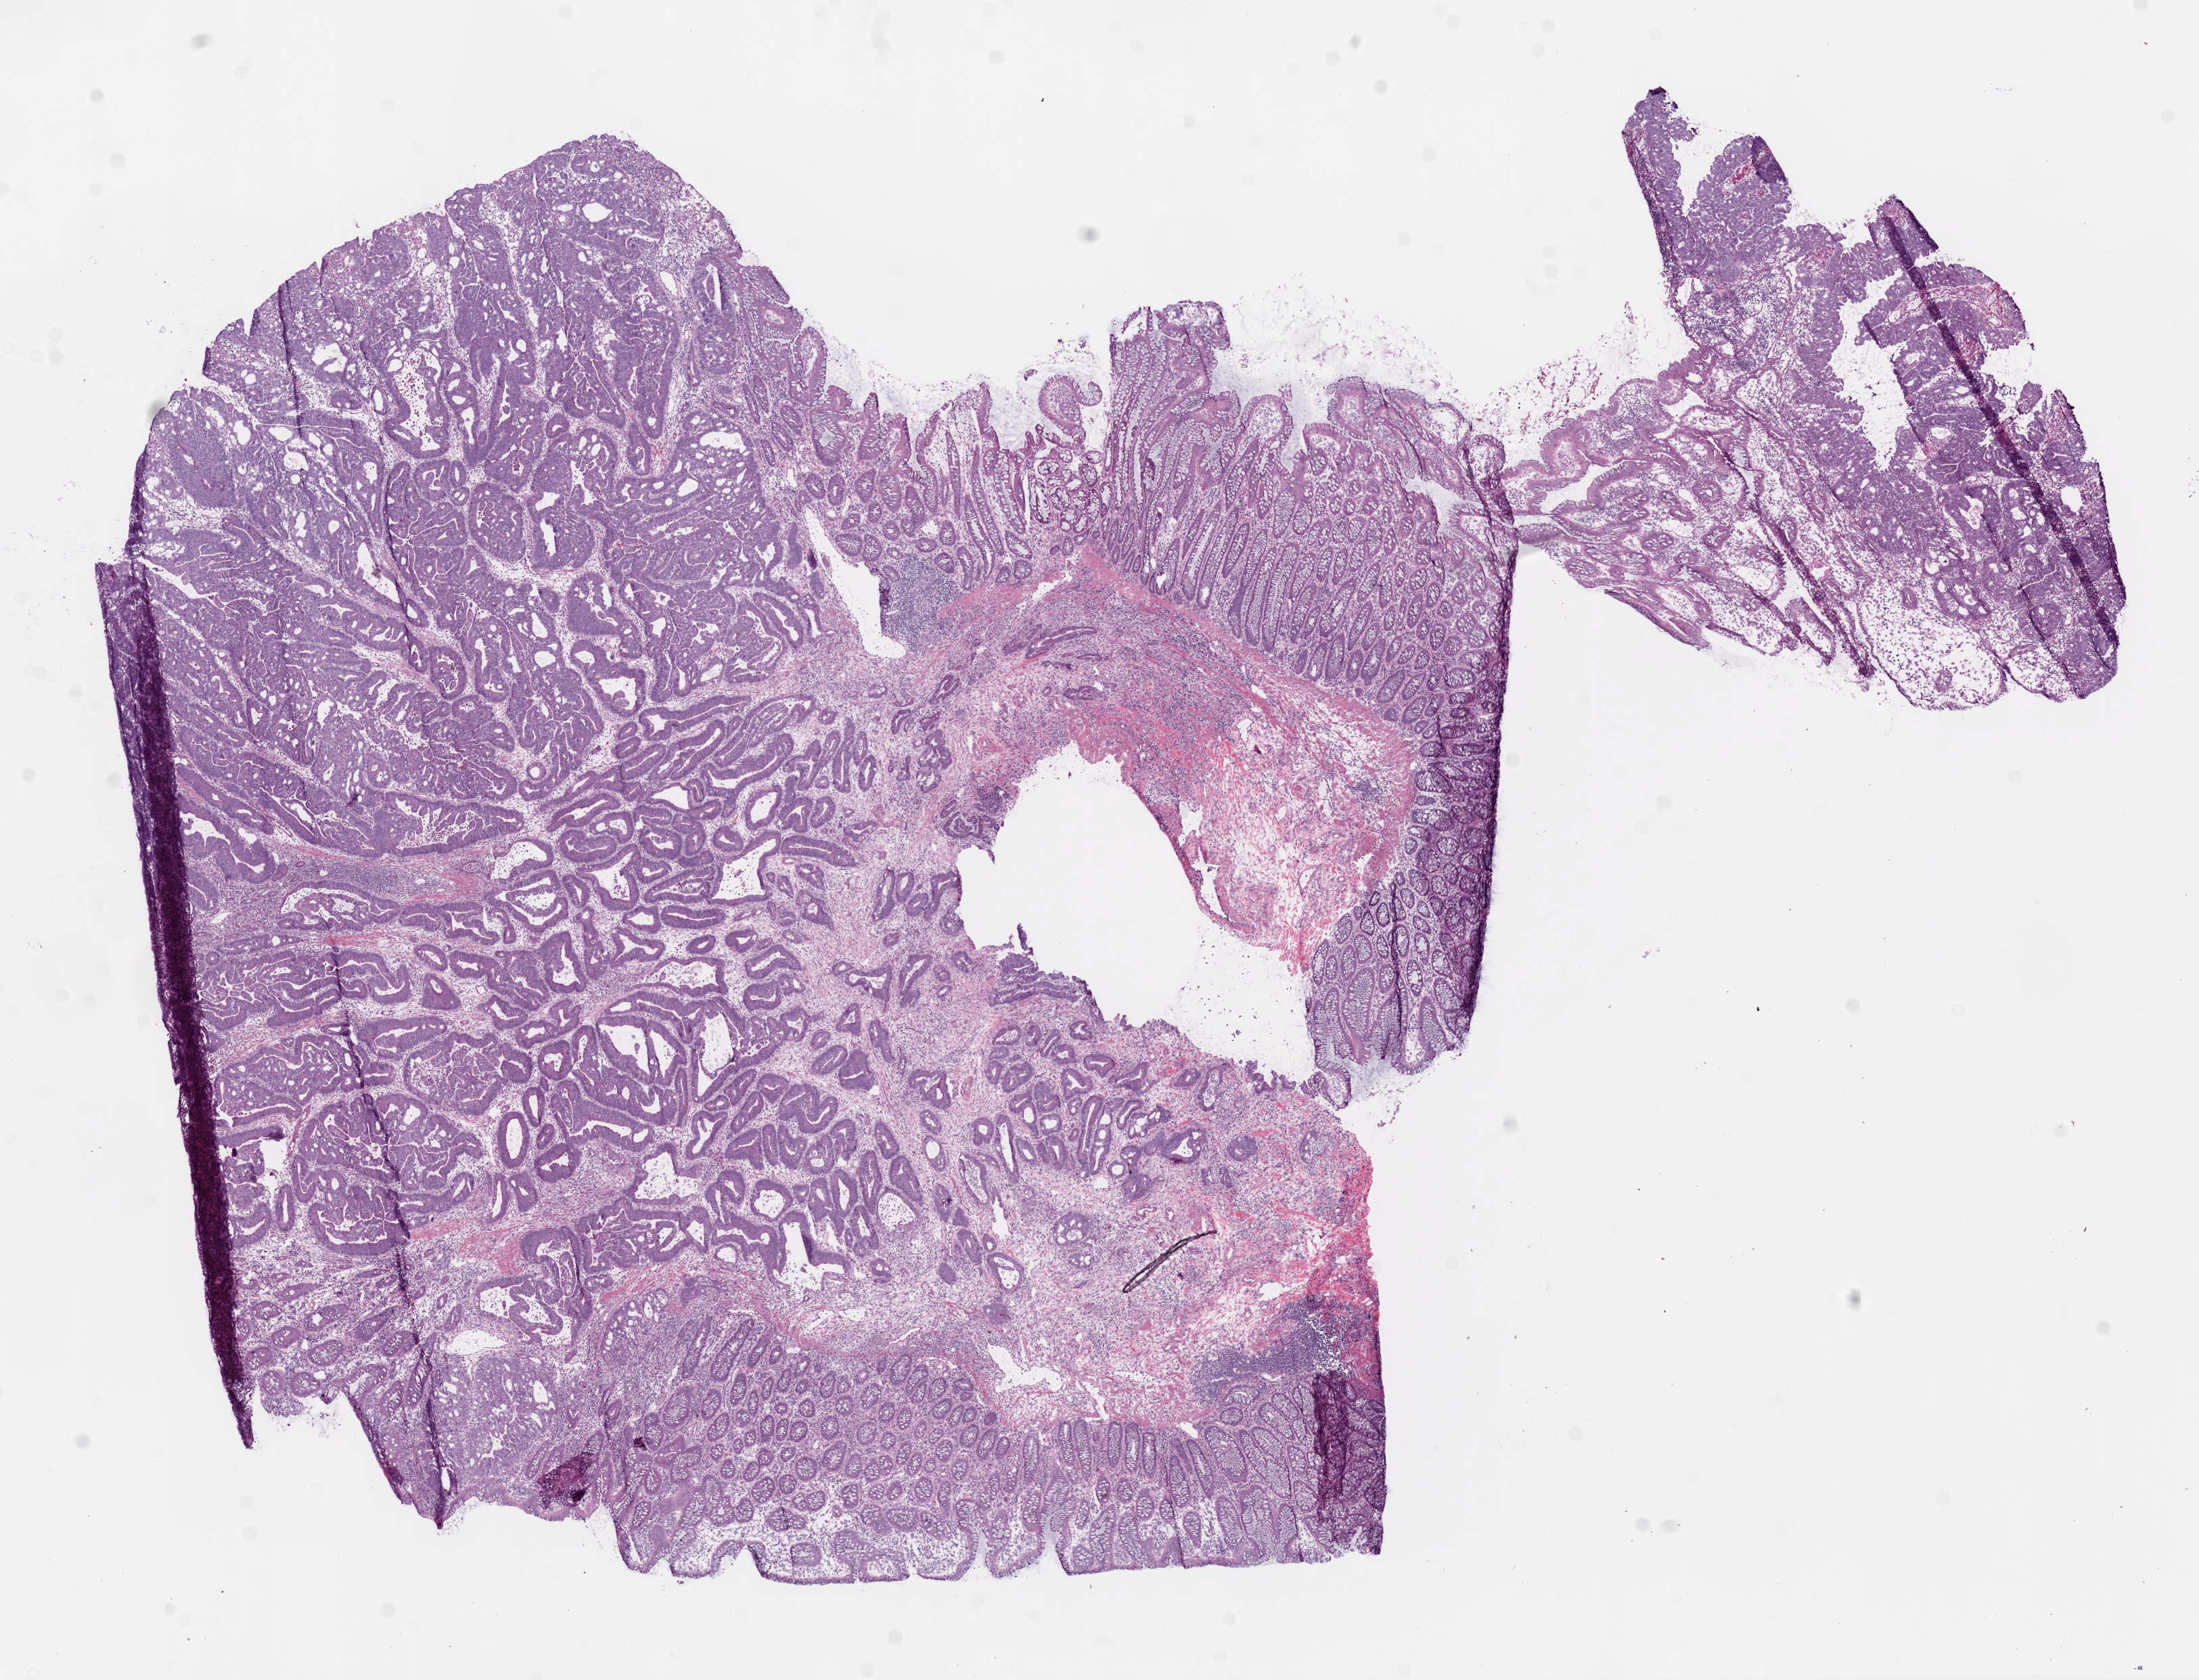
Whole-slide histology image, H&E, a low-resolution overview of the entire scanned area, about 13.0 x 10.0 mm; frozen section; sample: primary tumour, rectum. Male, age 75 years at initial diagnosis. Composition of this section per pathologist review: tumour cells 73%, tumour nuclei 65%, normal cells 15%, stromal cells 10%, necrosis 2%.
Histologic diagnosis: Adenocarcinoma, NOS (rectosigmoid junction). Lymph nodes positive (case pathology): 0 of 30 examined. AJCC pathologic stage: I (6th edition).